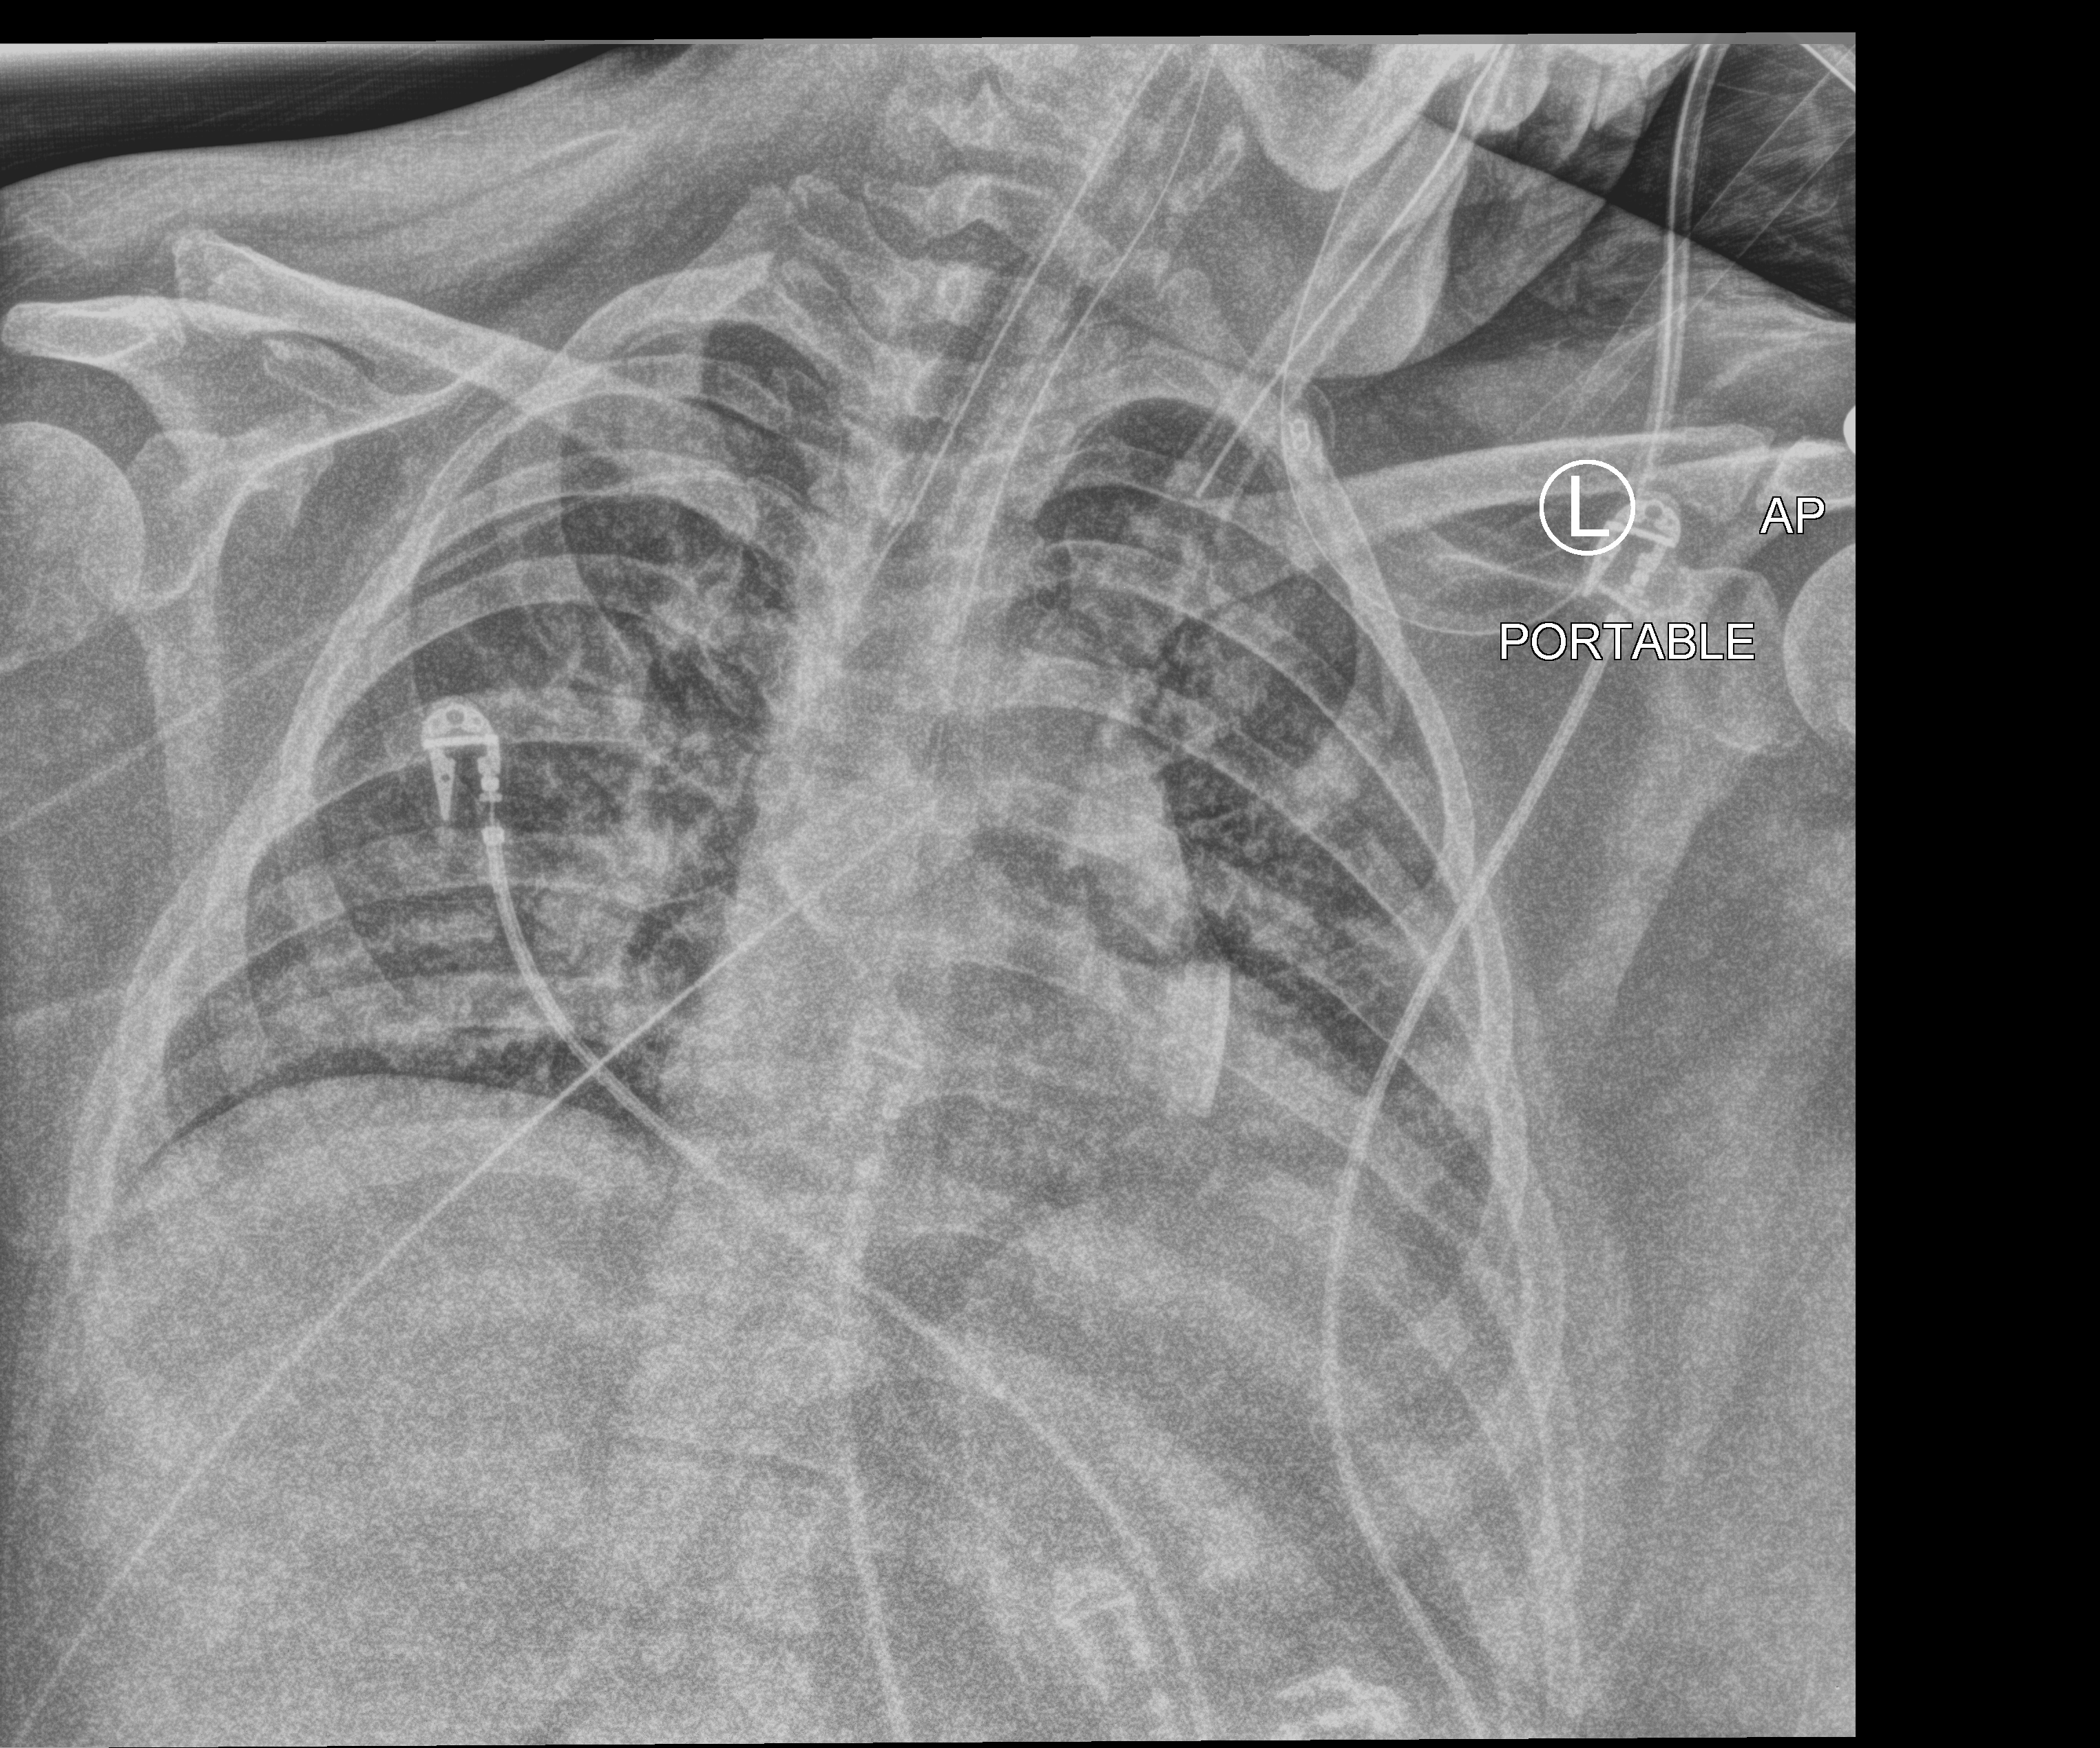
Portable chest radiograph, anteroposterior (AP) projection. Patient hospitalised with COVID-19; female, aged 18–59 years.
Hospital-stay facts (about this admission, not read from this image; timing relative to this image not recorded): admitted to intensive care during this hospital stay: yes; mechanically ventilated during this hospital stay: yes.